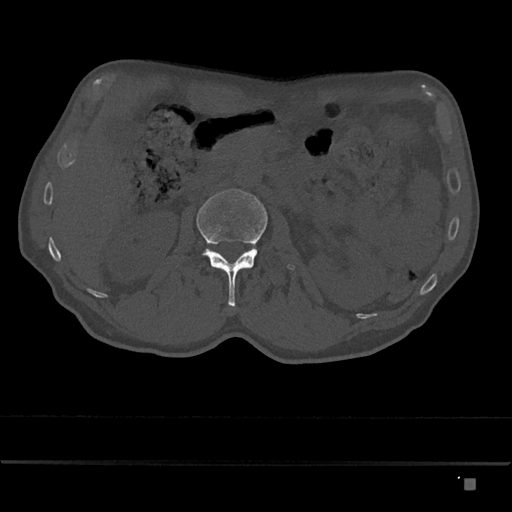
CT including the spine, one axial slice. Reconstruction kernel Br40s/3. 120 kVp. Bone window (W 1800 / L 400 HU). 0.5 mm slice thickness. 512 × 512 image matrix. Male patient, age 72 years. From the clinical record (not read from this slice): primary cancer: prostate.
Annotated regions visible in this slice (semi-automatic segmentation, software-assisted and operator-edited):
- L2 vertebra: bounding box [x1, y1, x2, y2] px = [196, 189, 295, 307]